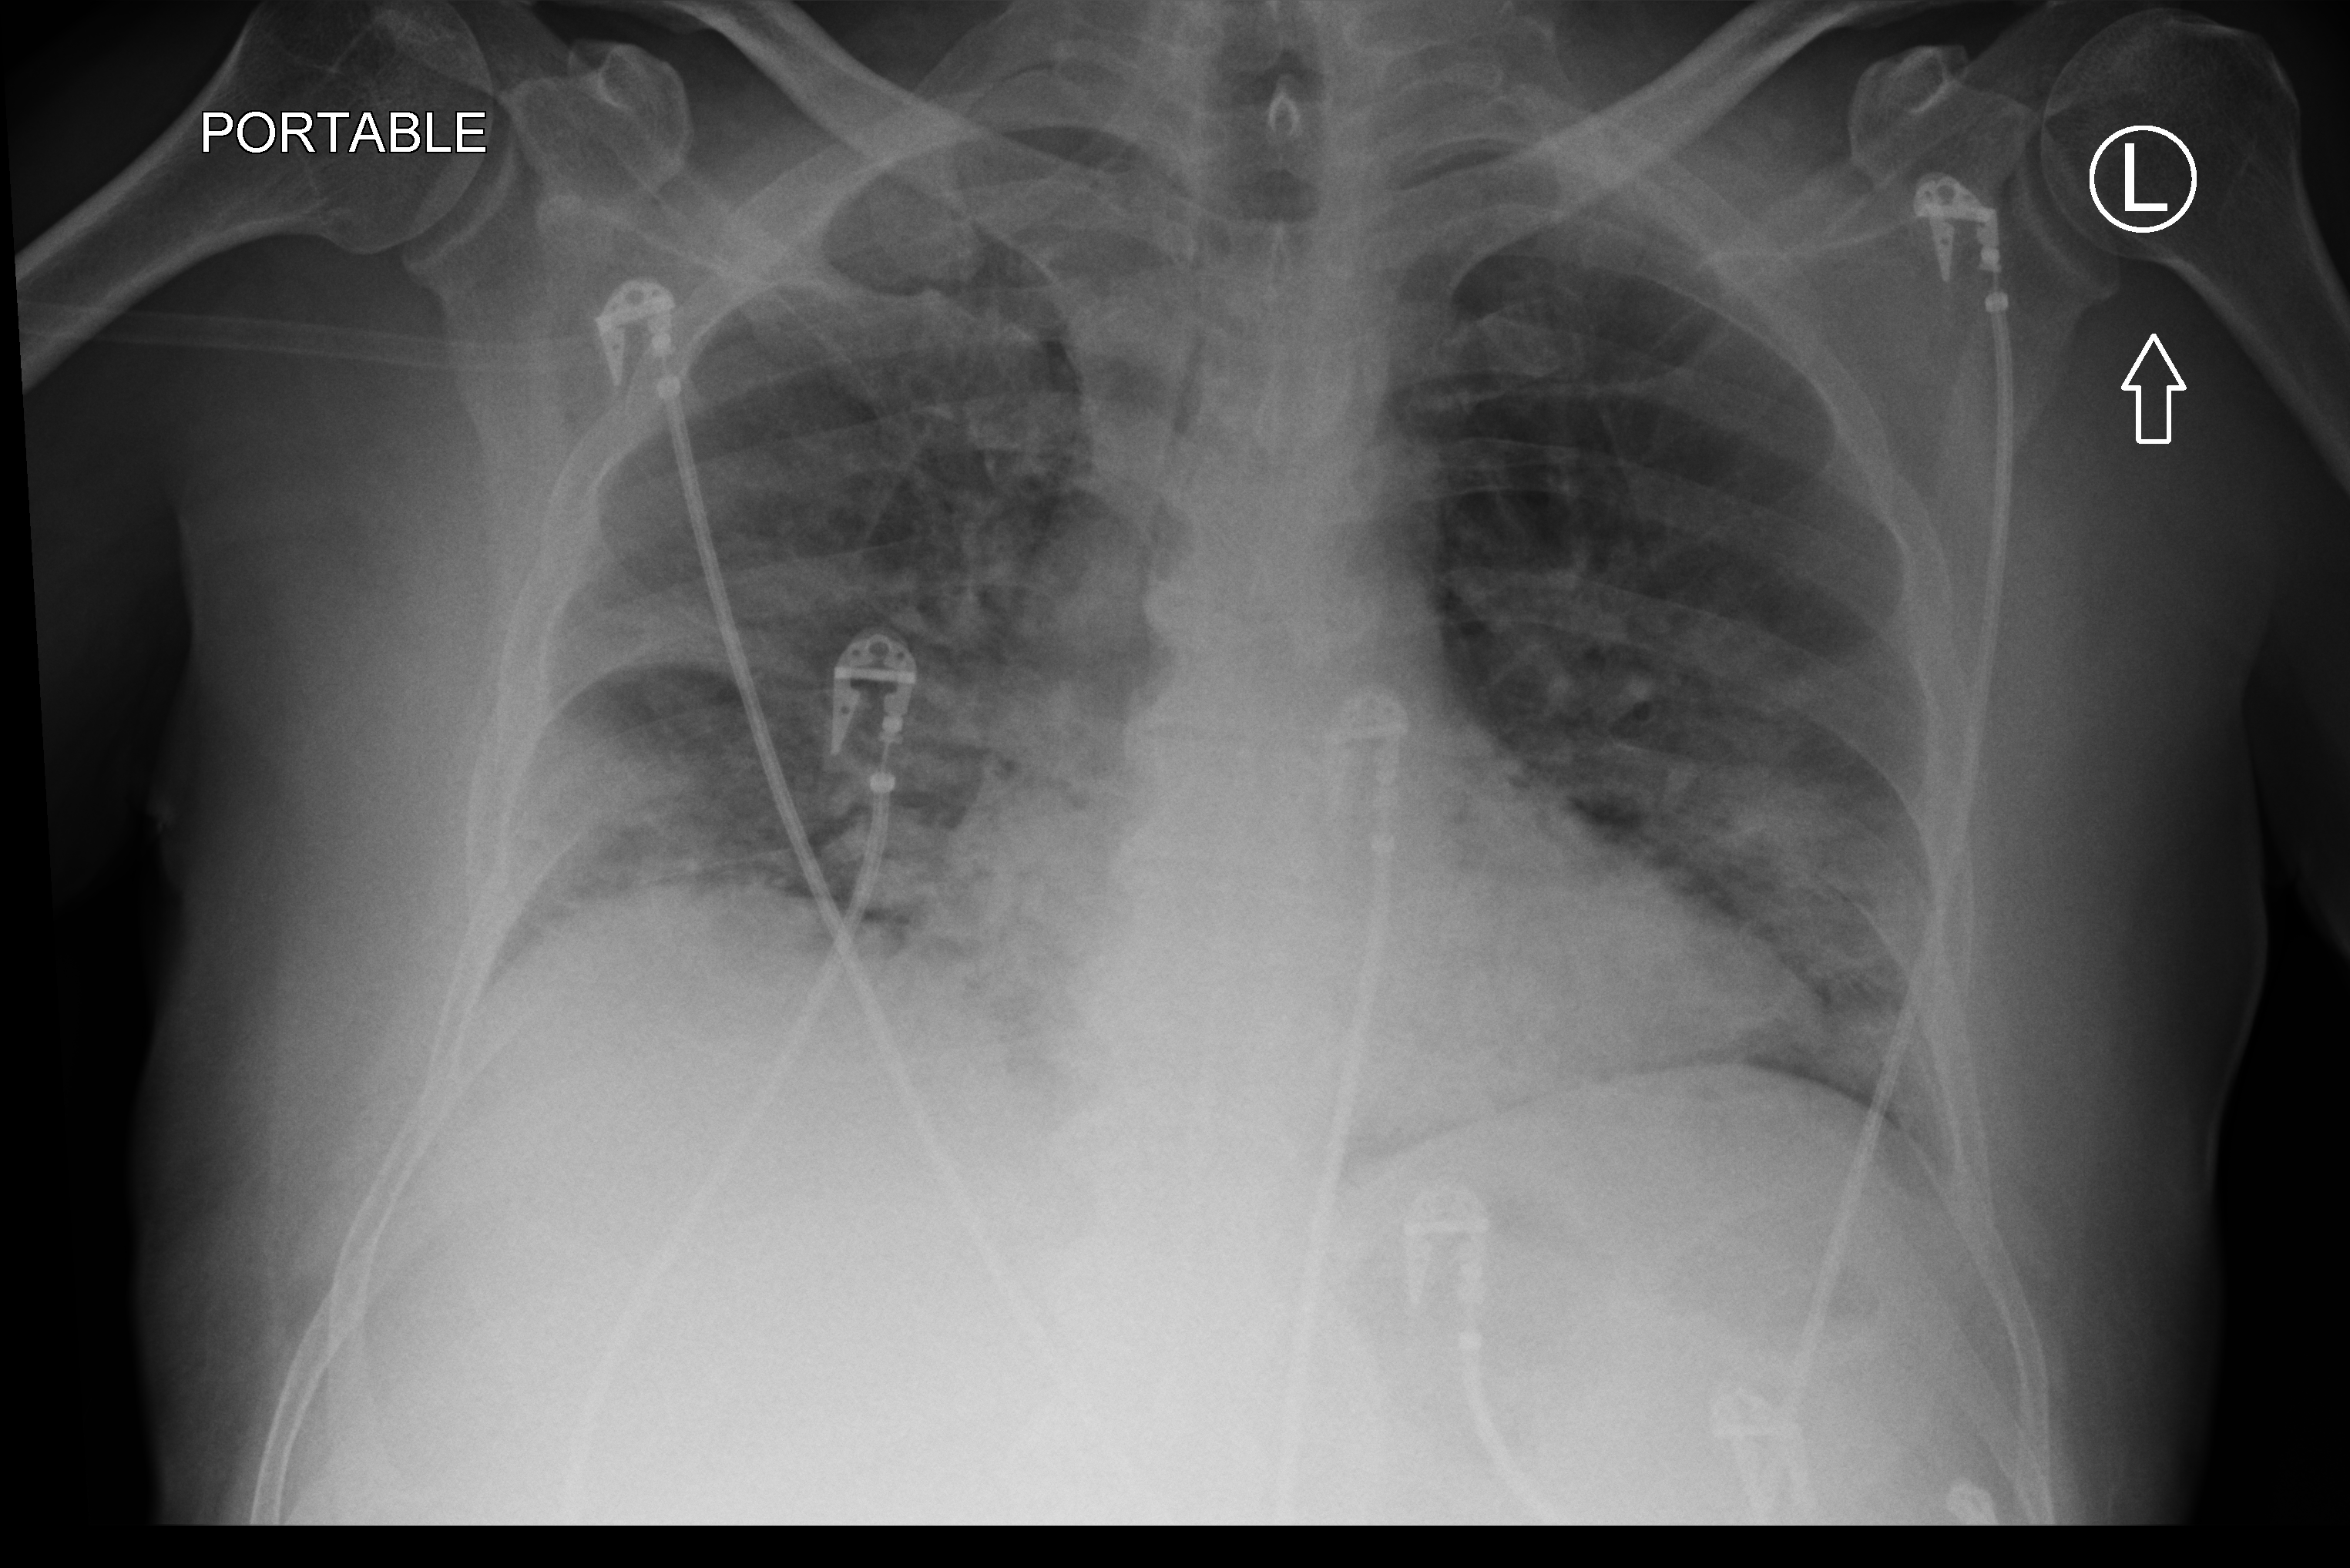
Bedside chest radiograph (computed radiography), anteroposterior (AP) projection. Male patient hospitalised with COVID-19, age 60–74 years.
Hospital-stay facts (about this admission, not read from this image; timing relative to this image not recorded): chronic kidney disease (admission record): no; admitted to intensive care during this hospital stay: yes; other chronic lung disease (admission record): no.